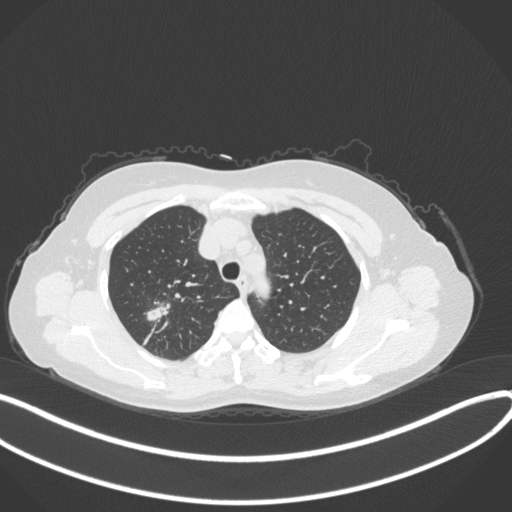
Chest CT, one axial slice. Position 286 of 342 along the scan axis. 120 kVp. Lung window (W 1500 / L -600 HU). 512 × 512 image matrix, field of view 400 × 400 mm. Female patient, age 50 years. From the clinical record (not read from this slice): clinical TNM (as recorded): T1c N0 M0.
Structures marked on this image (rectangle marked by the reading radiologist):
- lung tumour (recorded histology: adenocarcinoma): bounding box (x1, y1, x2, y2) in pixels: (140, 298, 170, 327)